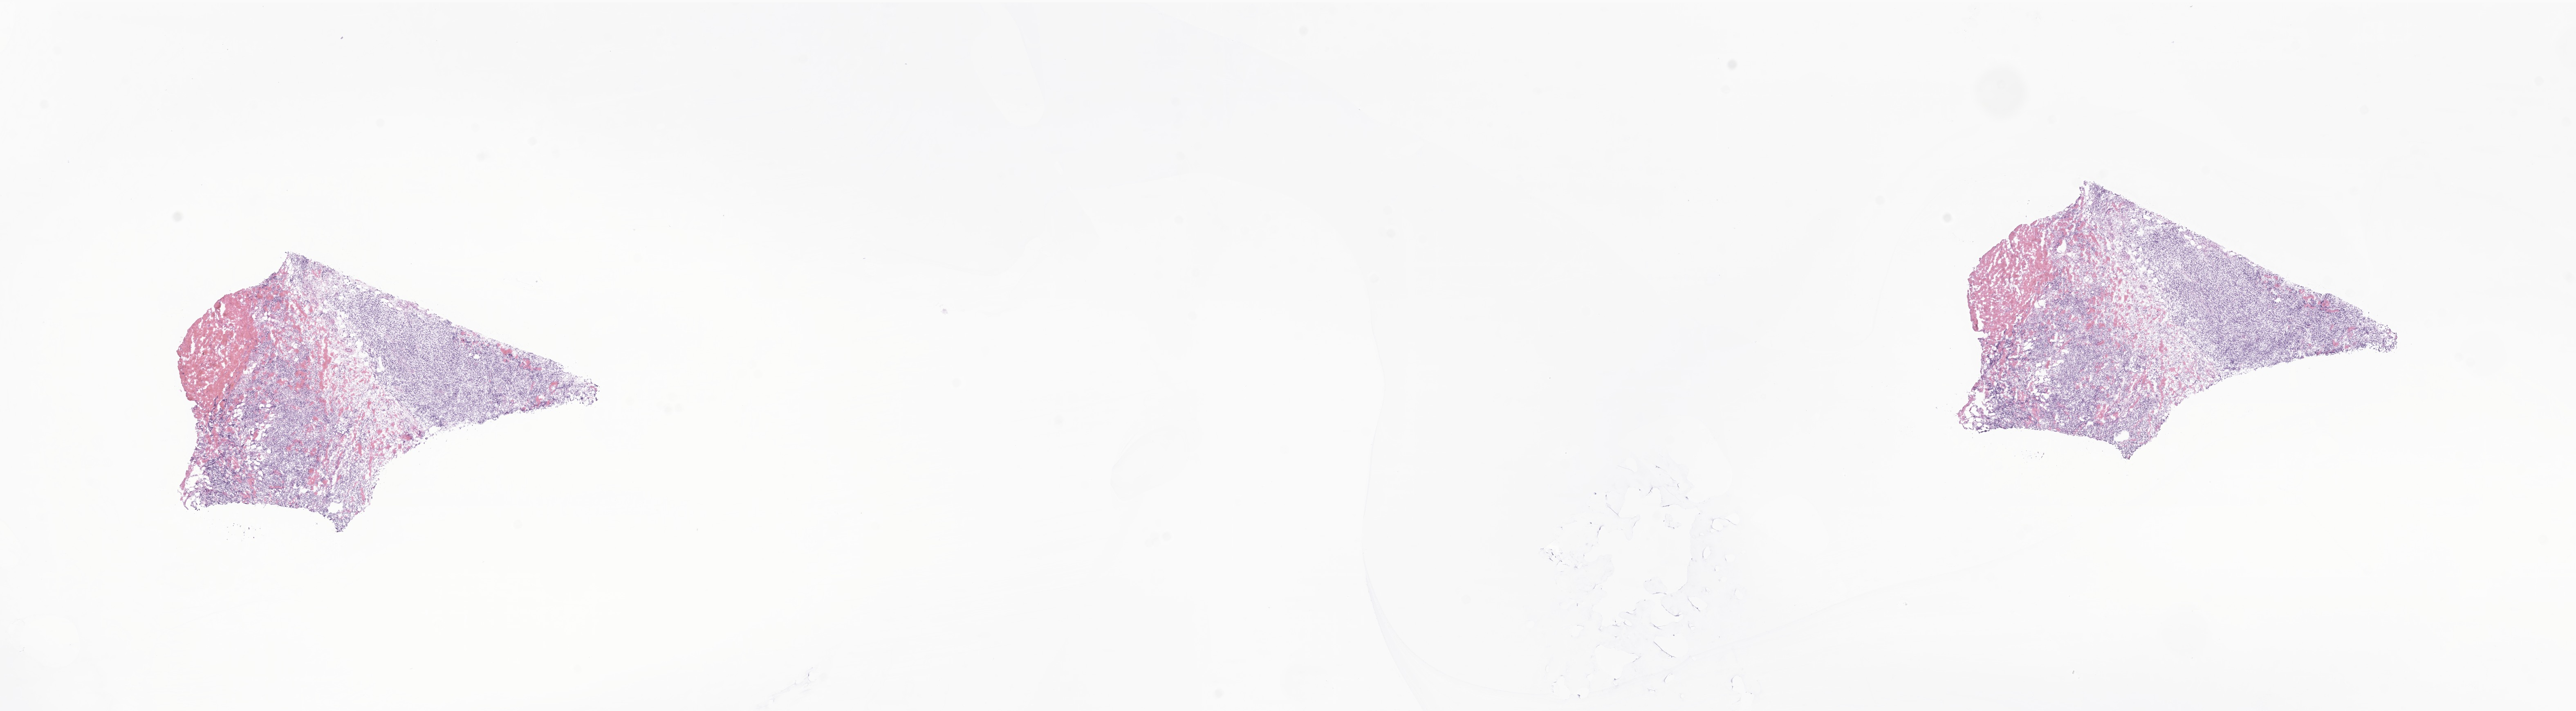
H&E whole-slide image of tumor tissue from the middle ear, whole scanned area (about 26.6 x 7.3 mm) shown as a low-resolution overview, frozen section (OCT-embedded). Patient male; age 68 months (5 years 8 months).
Diagnosis (ICD-O-3 morphology term): Desmoplastic small round cell tumor.